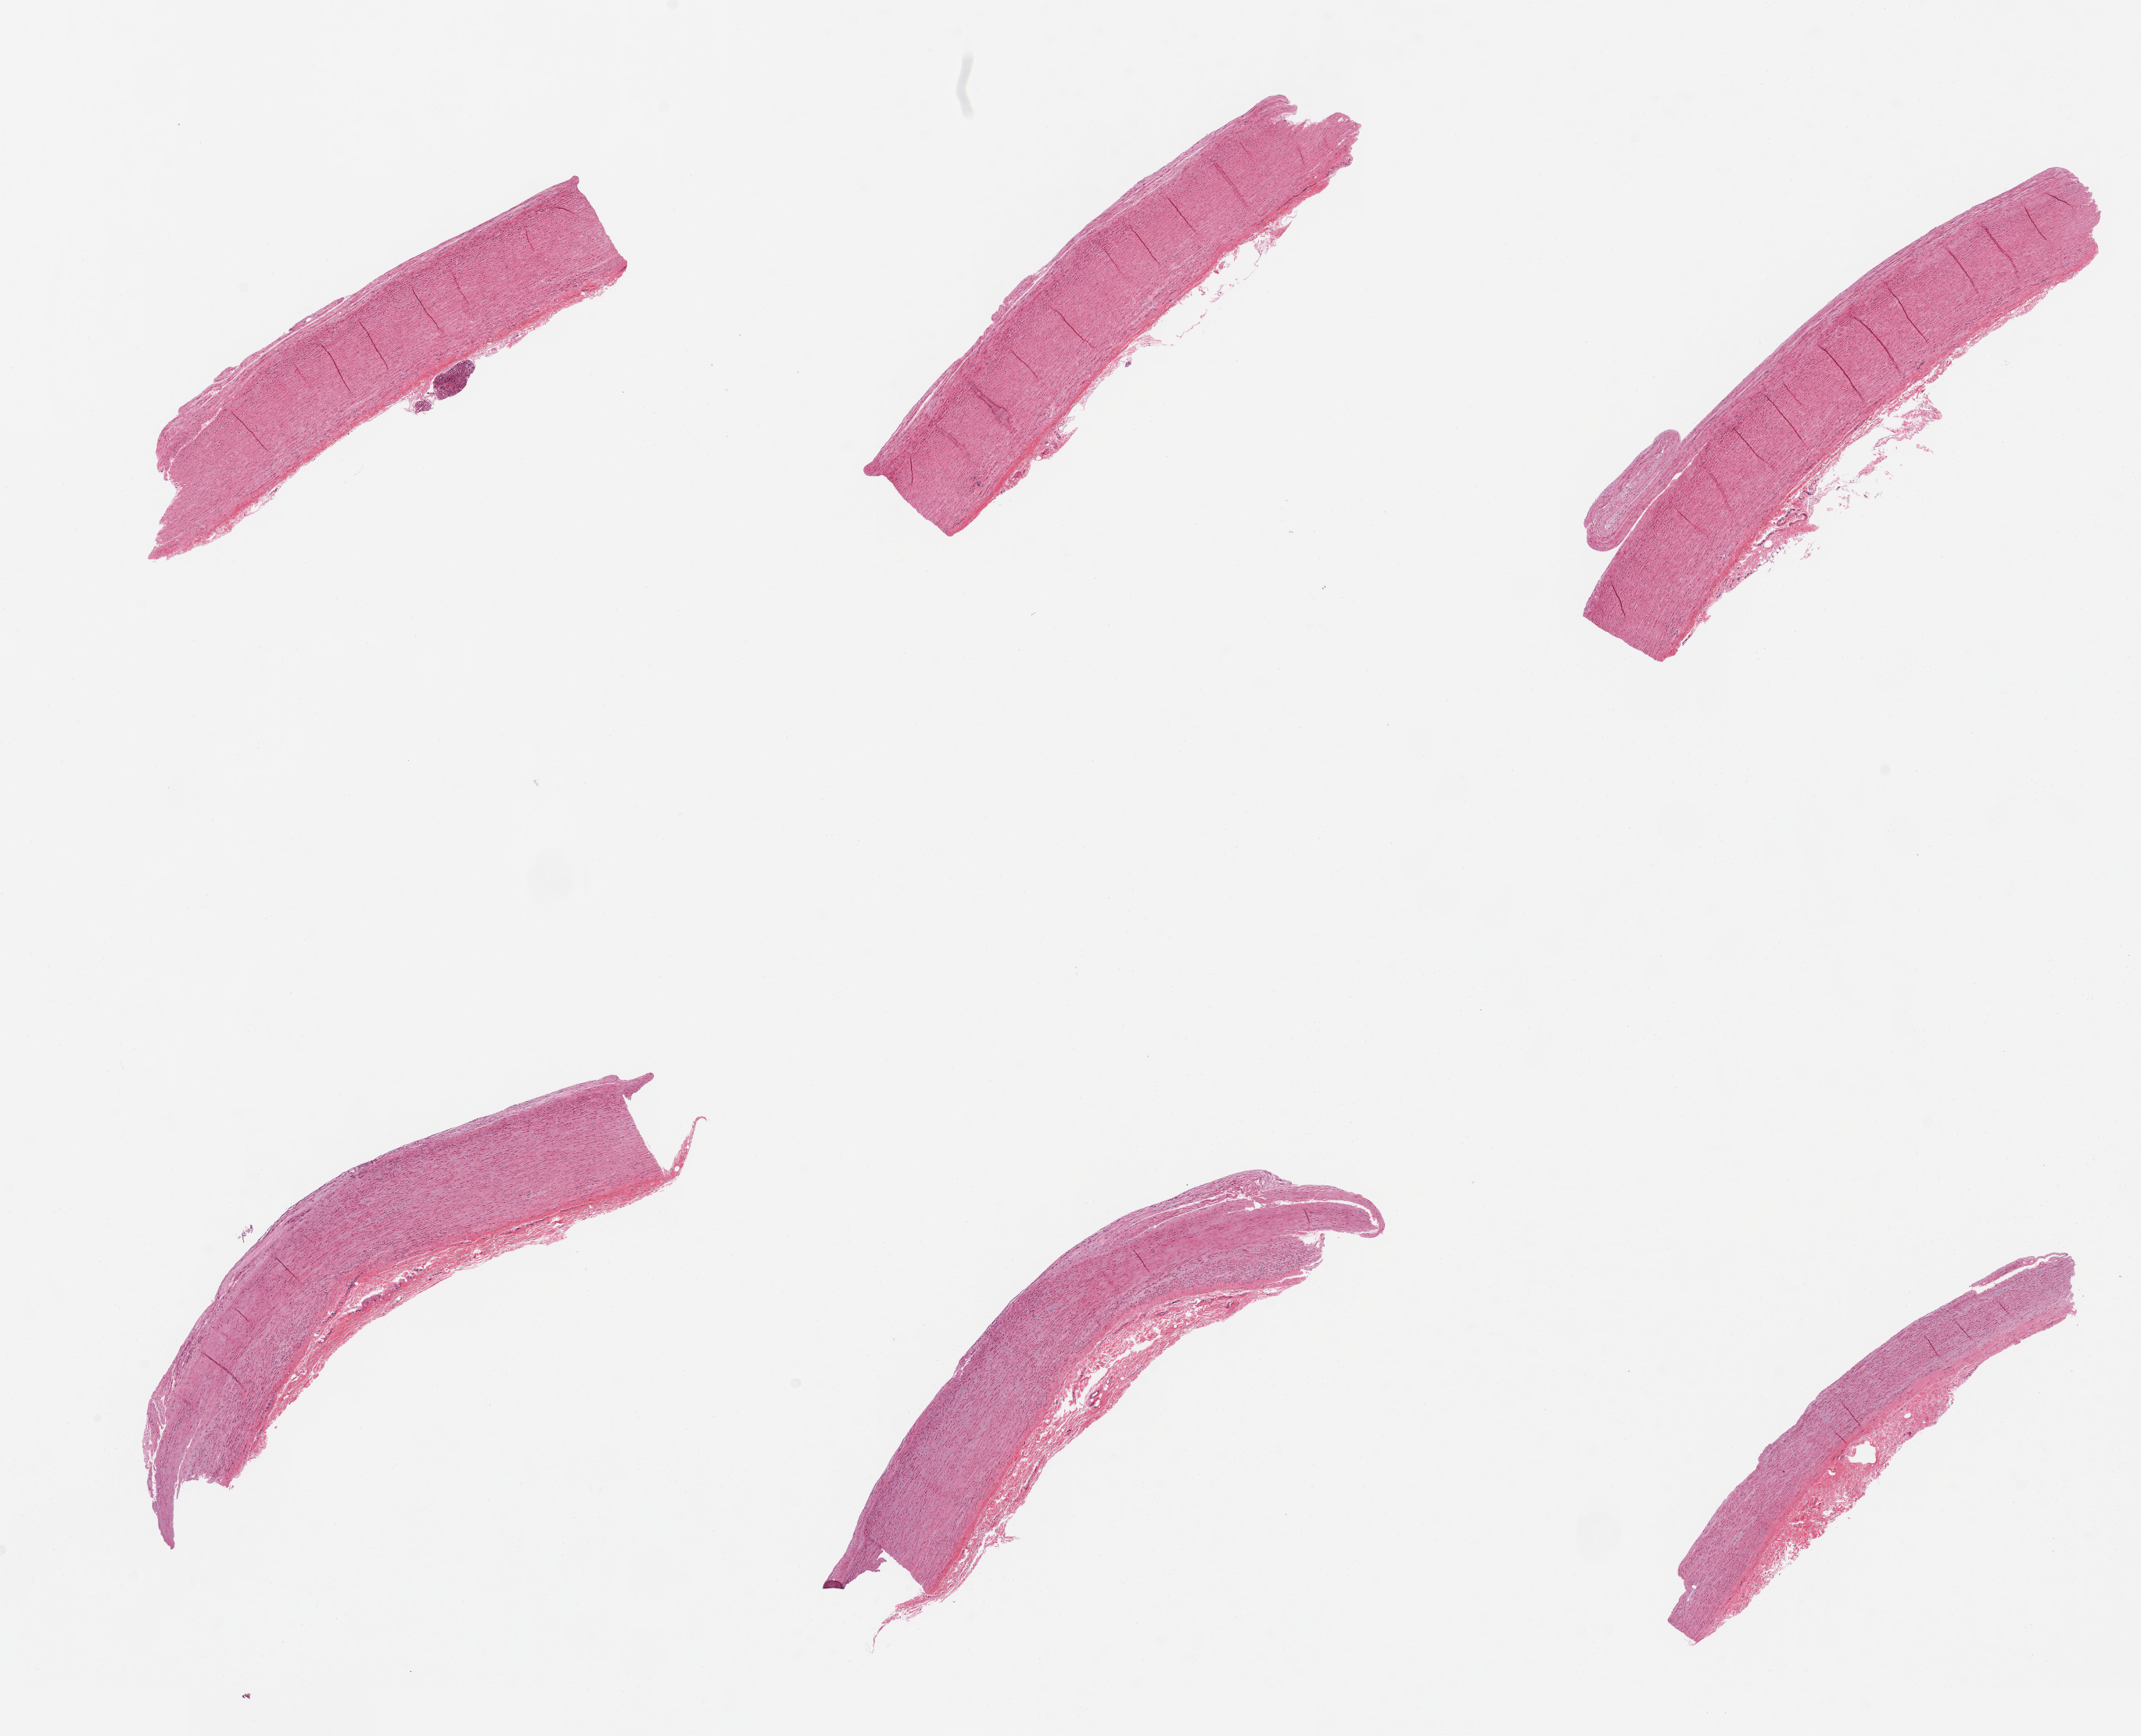
Haematoxylin and eosin whole-slide image — shown as a low-resolution overview of the whole scanned area (about 21.7 x 17.6 mm, from a 20x scan). PAXgene-fixed, paraffin-embedded tissue. Sampled site (target tissue): aorta. Tissue donor sample.
Reviewer comment on this tissue sample: 6 pieces, minimal atherosis.